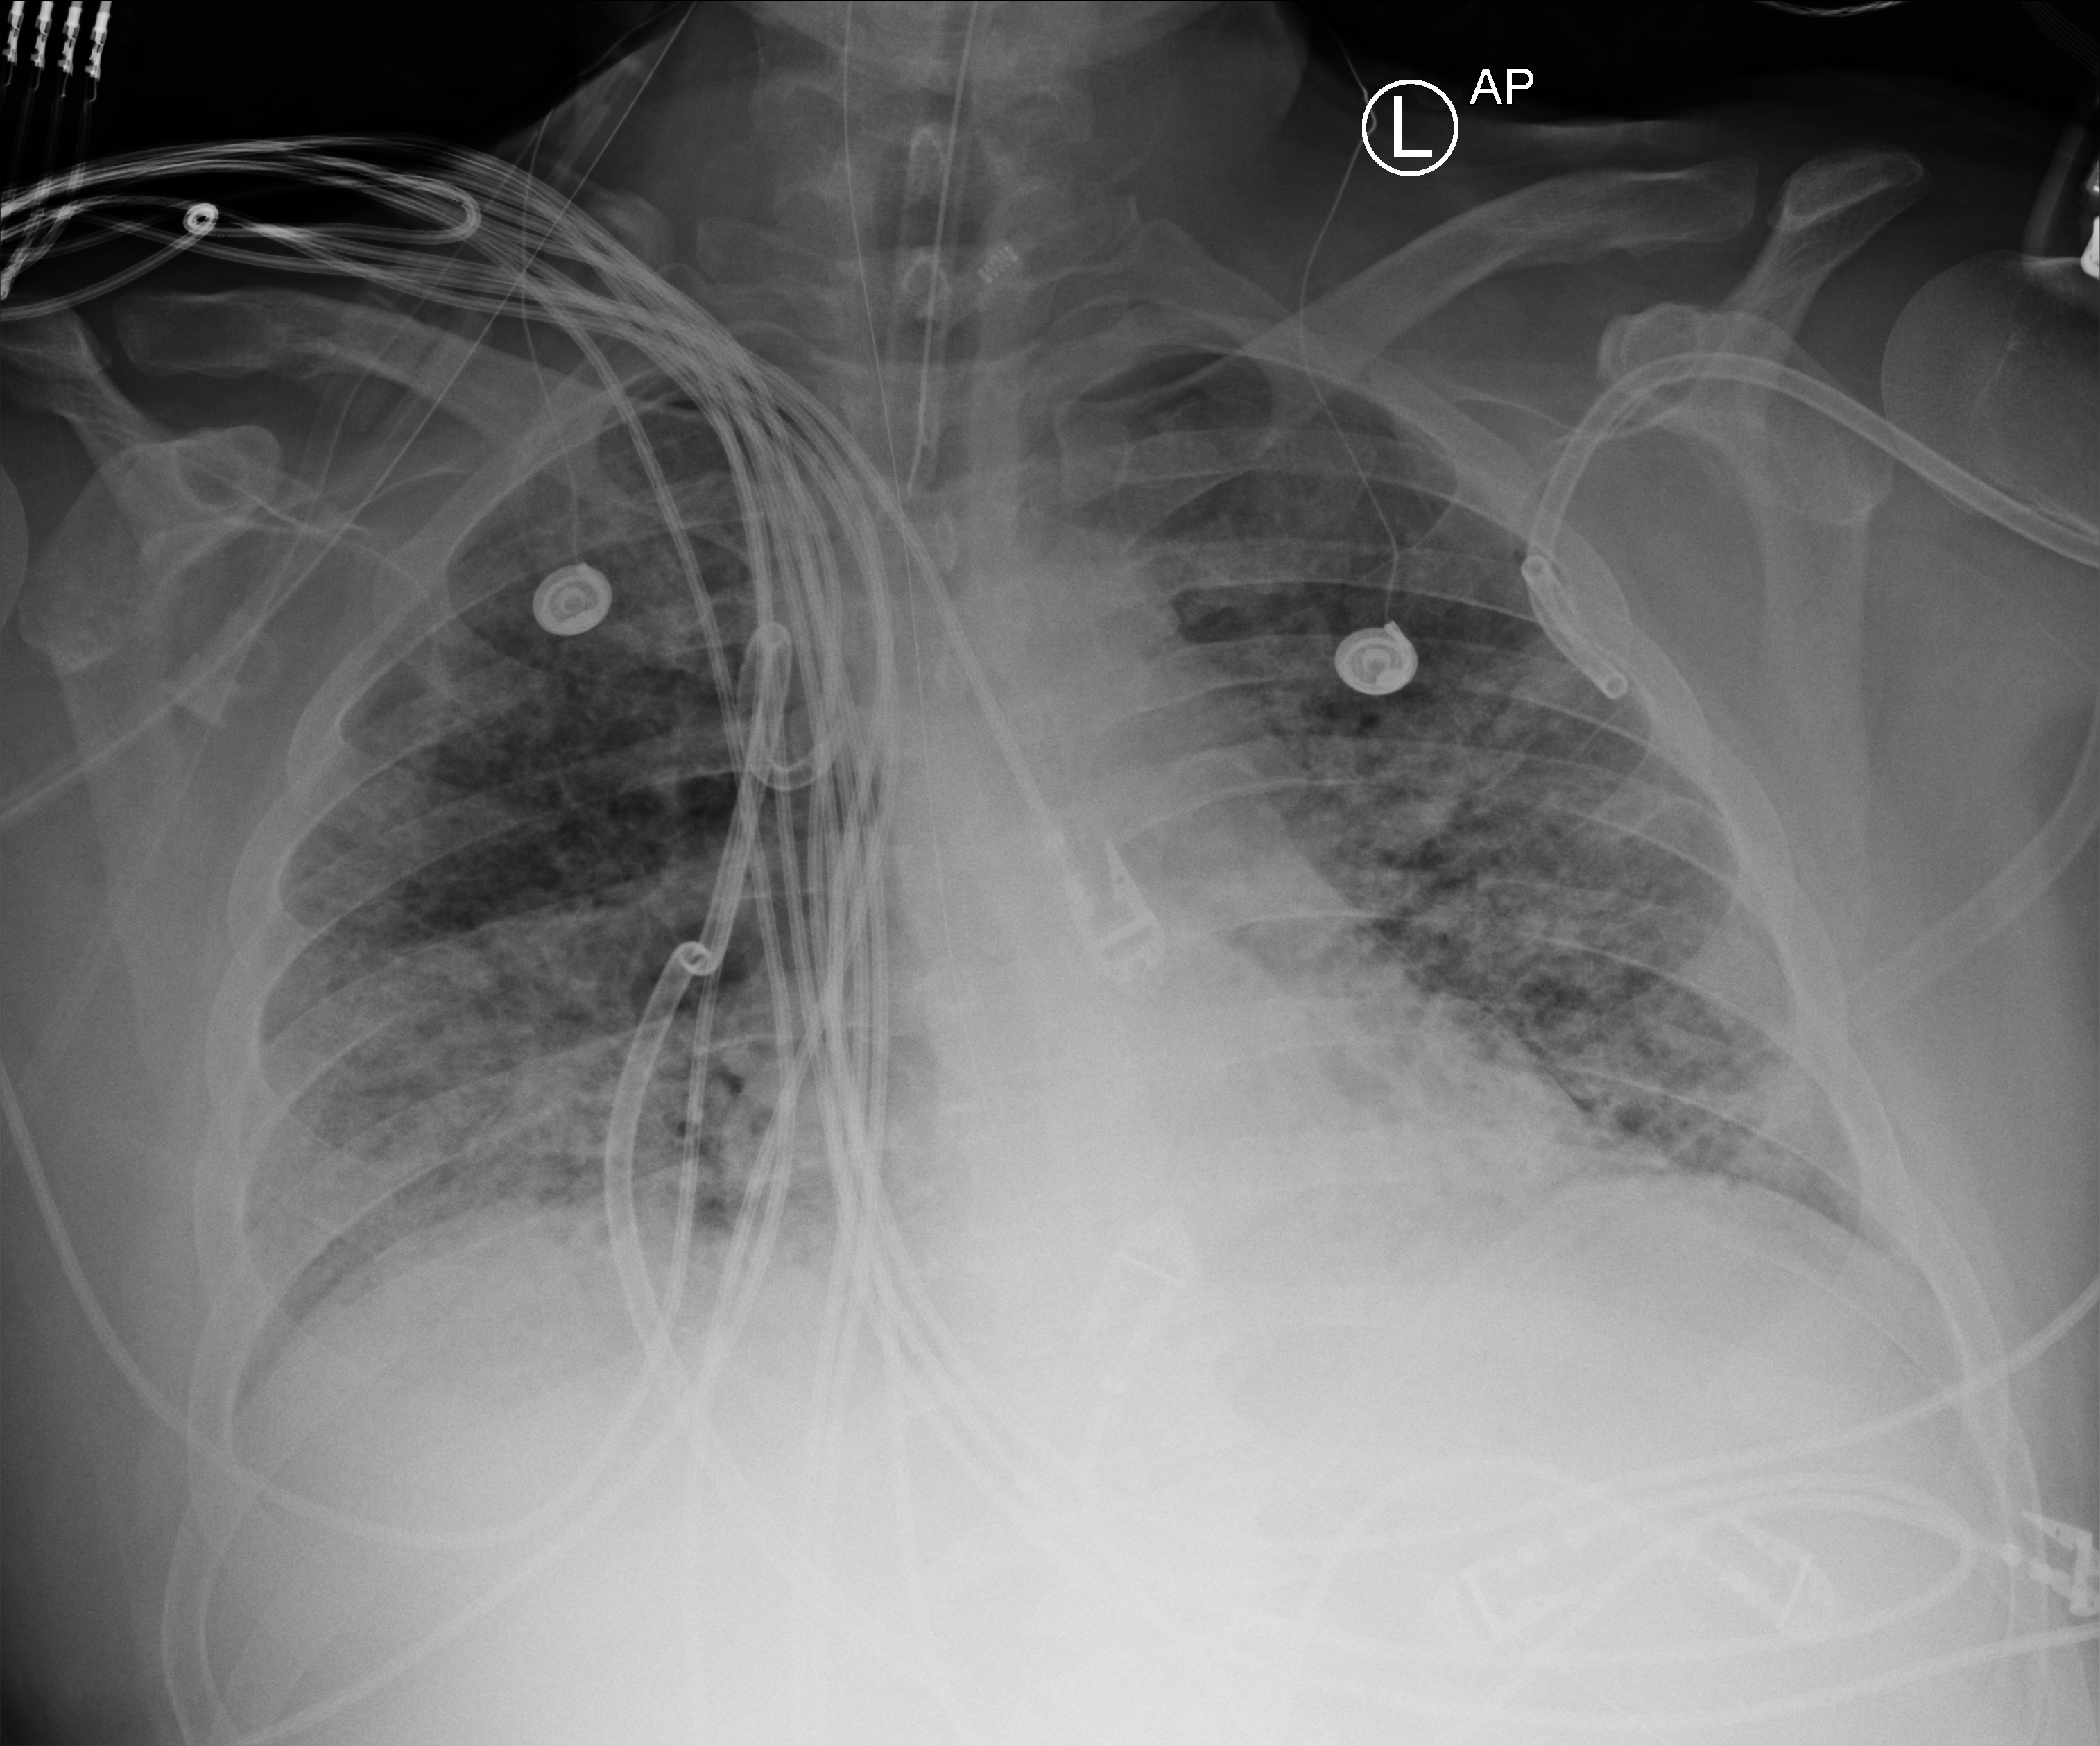
Bedside chest radiograph (computed radiography), anteroposterior (AP) projection. Adult patient hospitalised with COVID-19, age 18–59 years.
From the hospital-stay record, not from the radiograph (when in the stay this image was taken is not recorded): length of hospital stay: 31 days; mechanically ventilated during this hospital stay: yes.